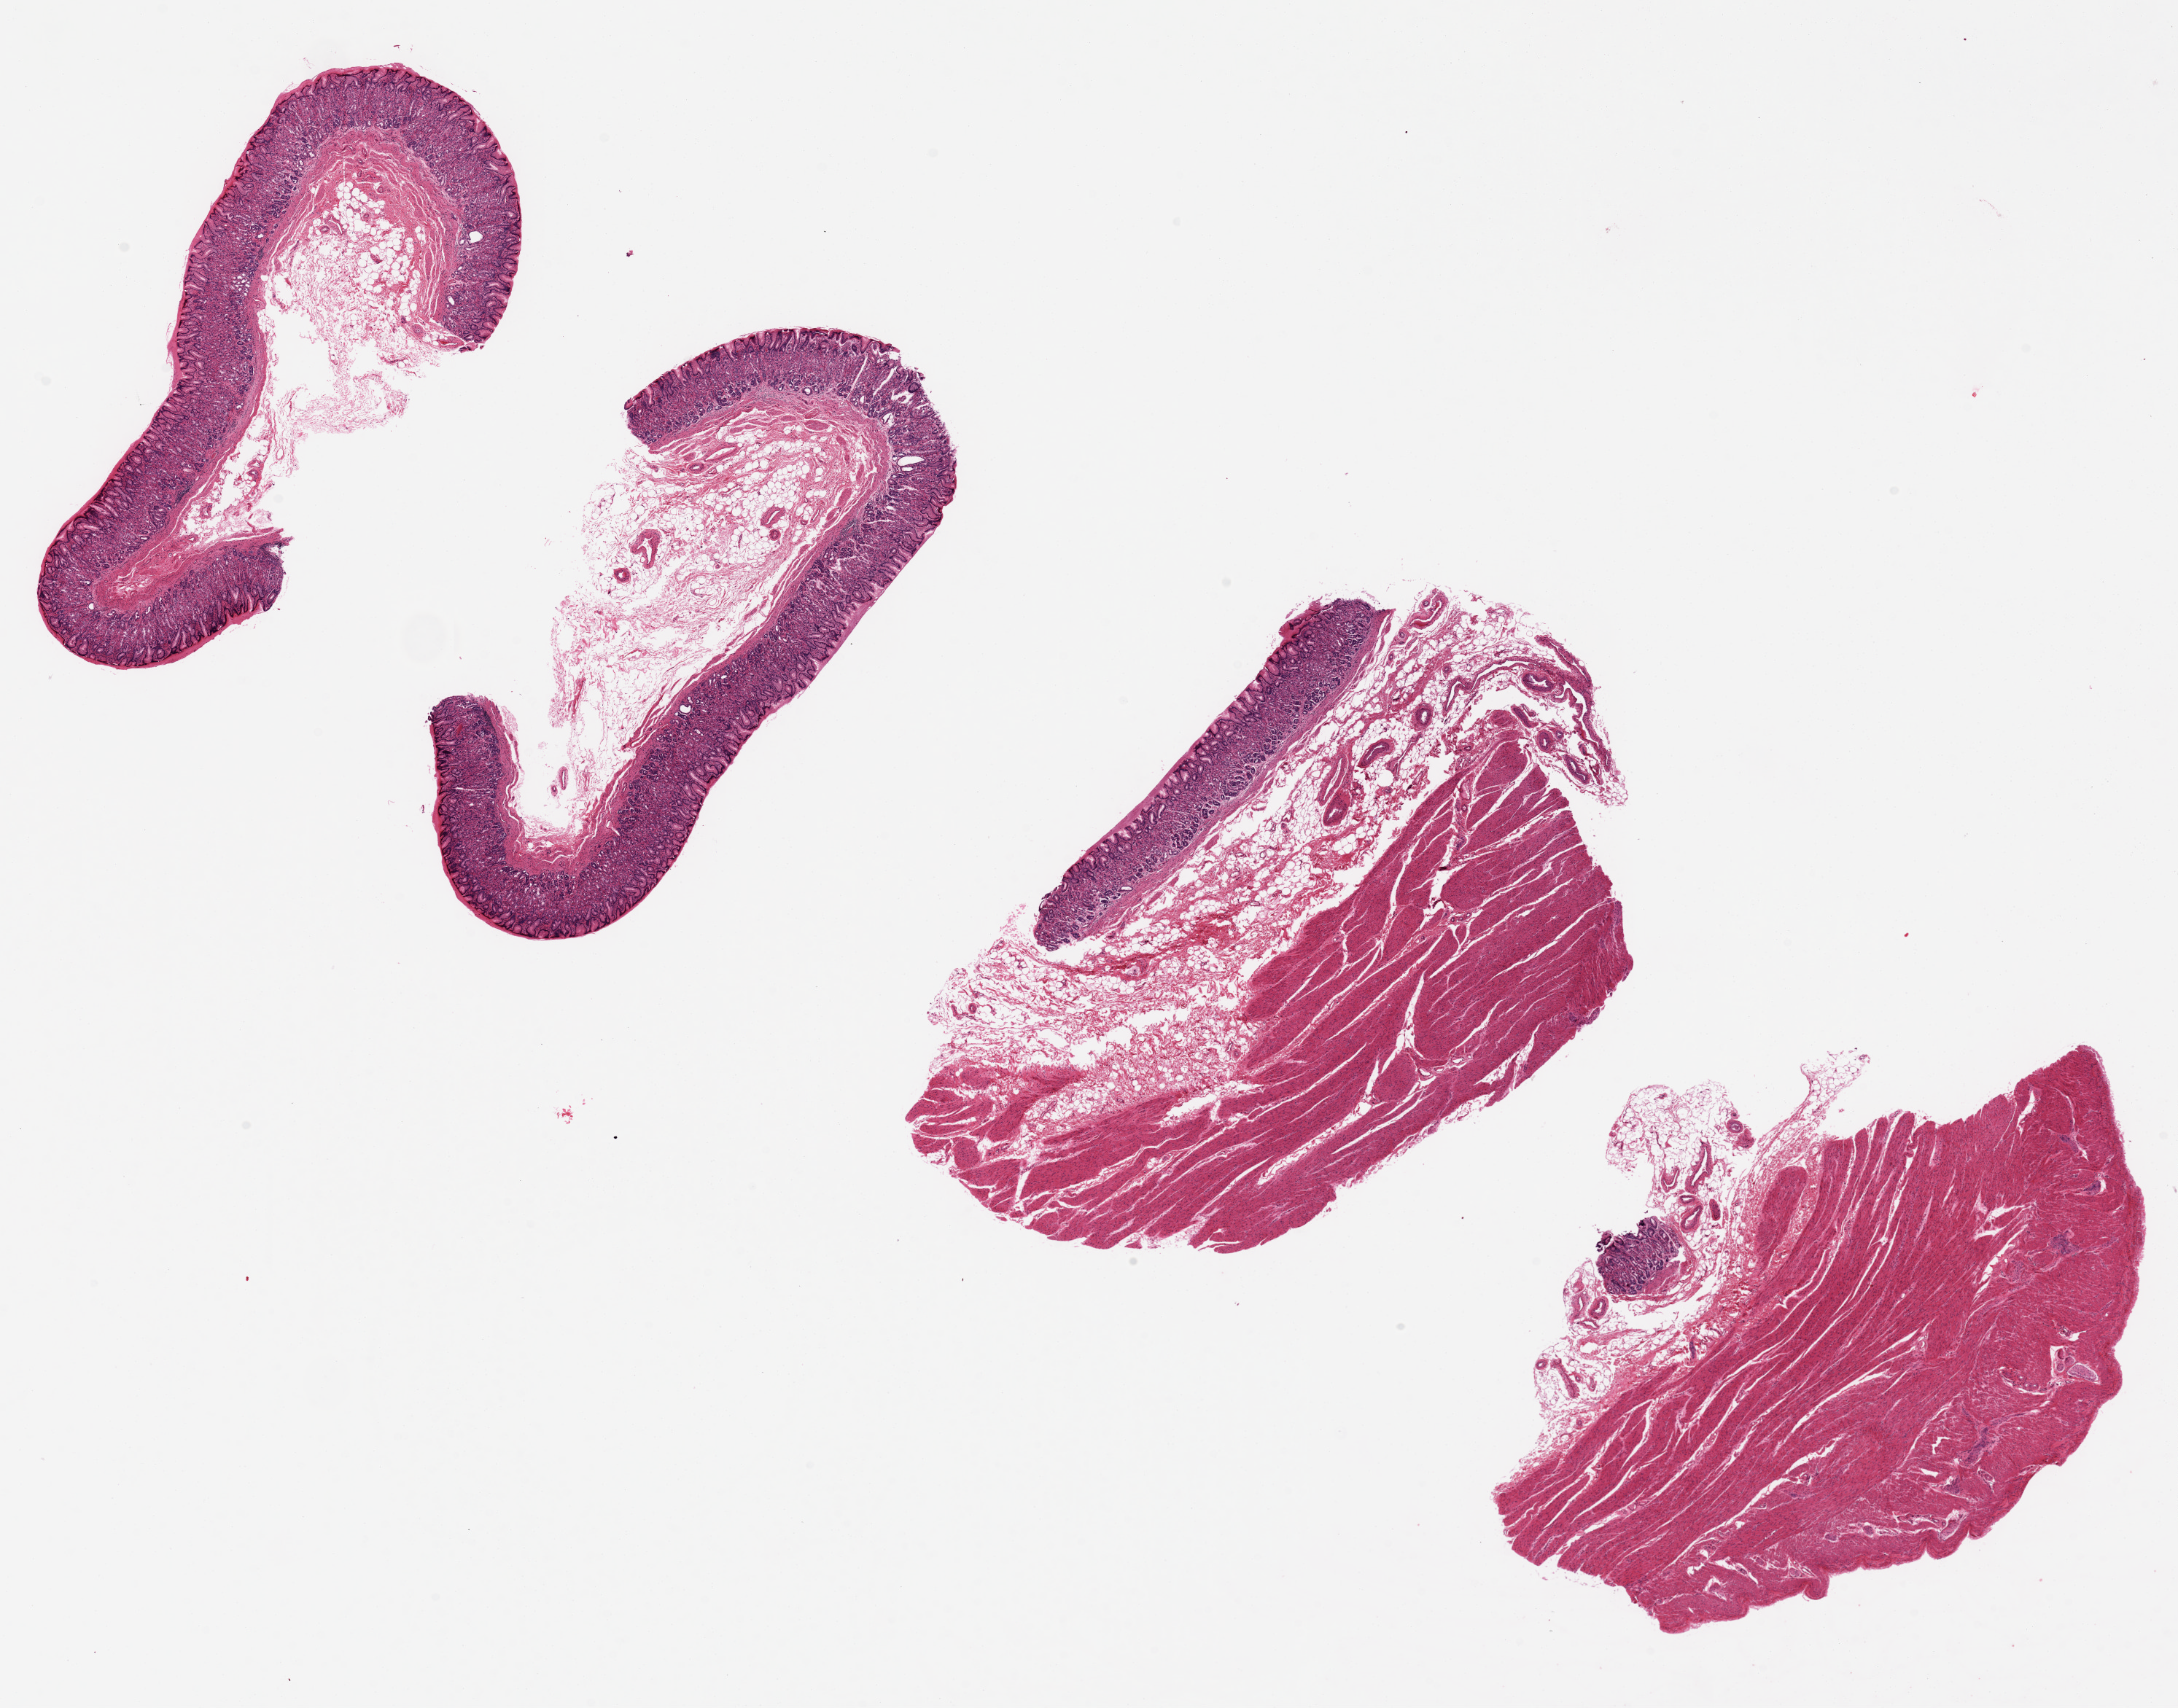
Digitized H&E-stained section — shown as a low-resolution overview of the whole scanned area (about 23.6 x 18.5 mm); PAXgene-fixed paraffin-embedded (PFPE) section; target tissue: stomach; tissue donor sample. Donor: male.
• review note (as recorded): Extremely well preserved. 1 of 4 pieces with little-no mucosa, which averages .8mm thickness in 3 pieces???two of which are 30-50%mucosa in thickness. Focal adipose areas underfixed